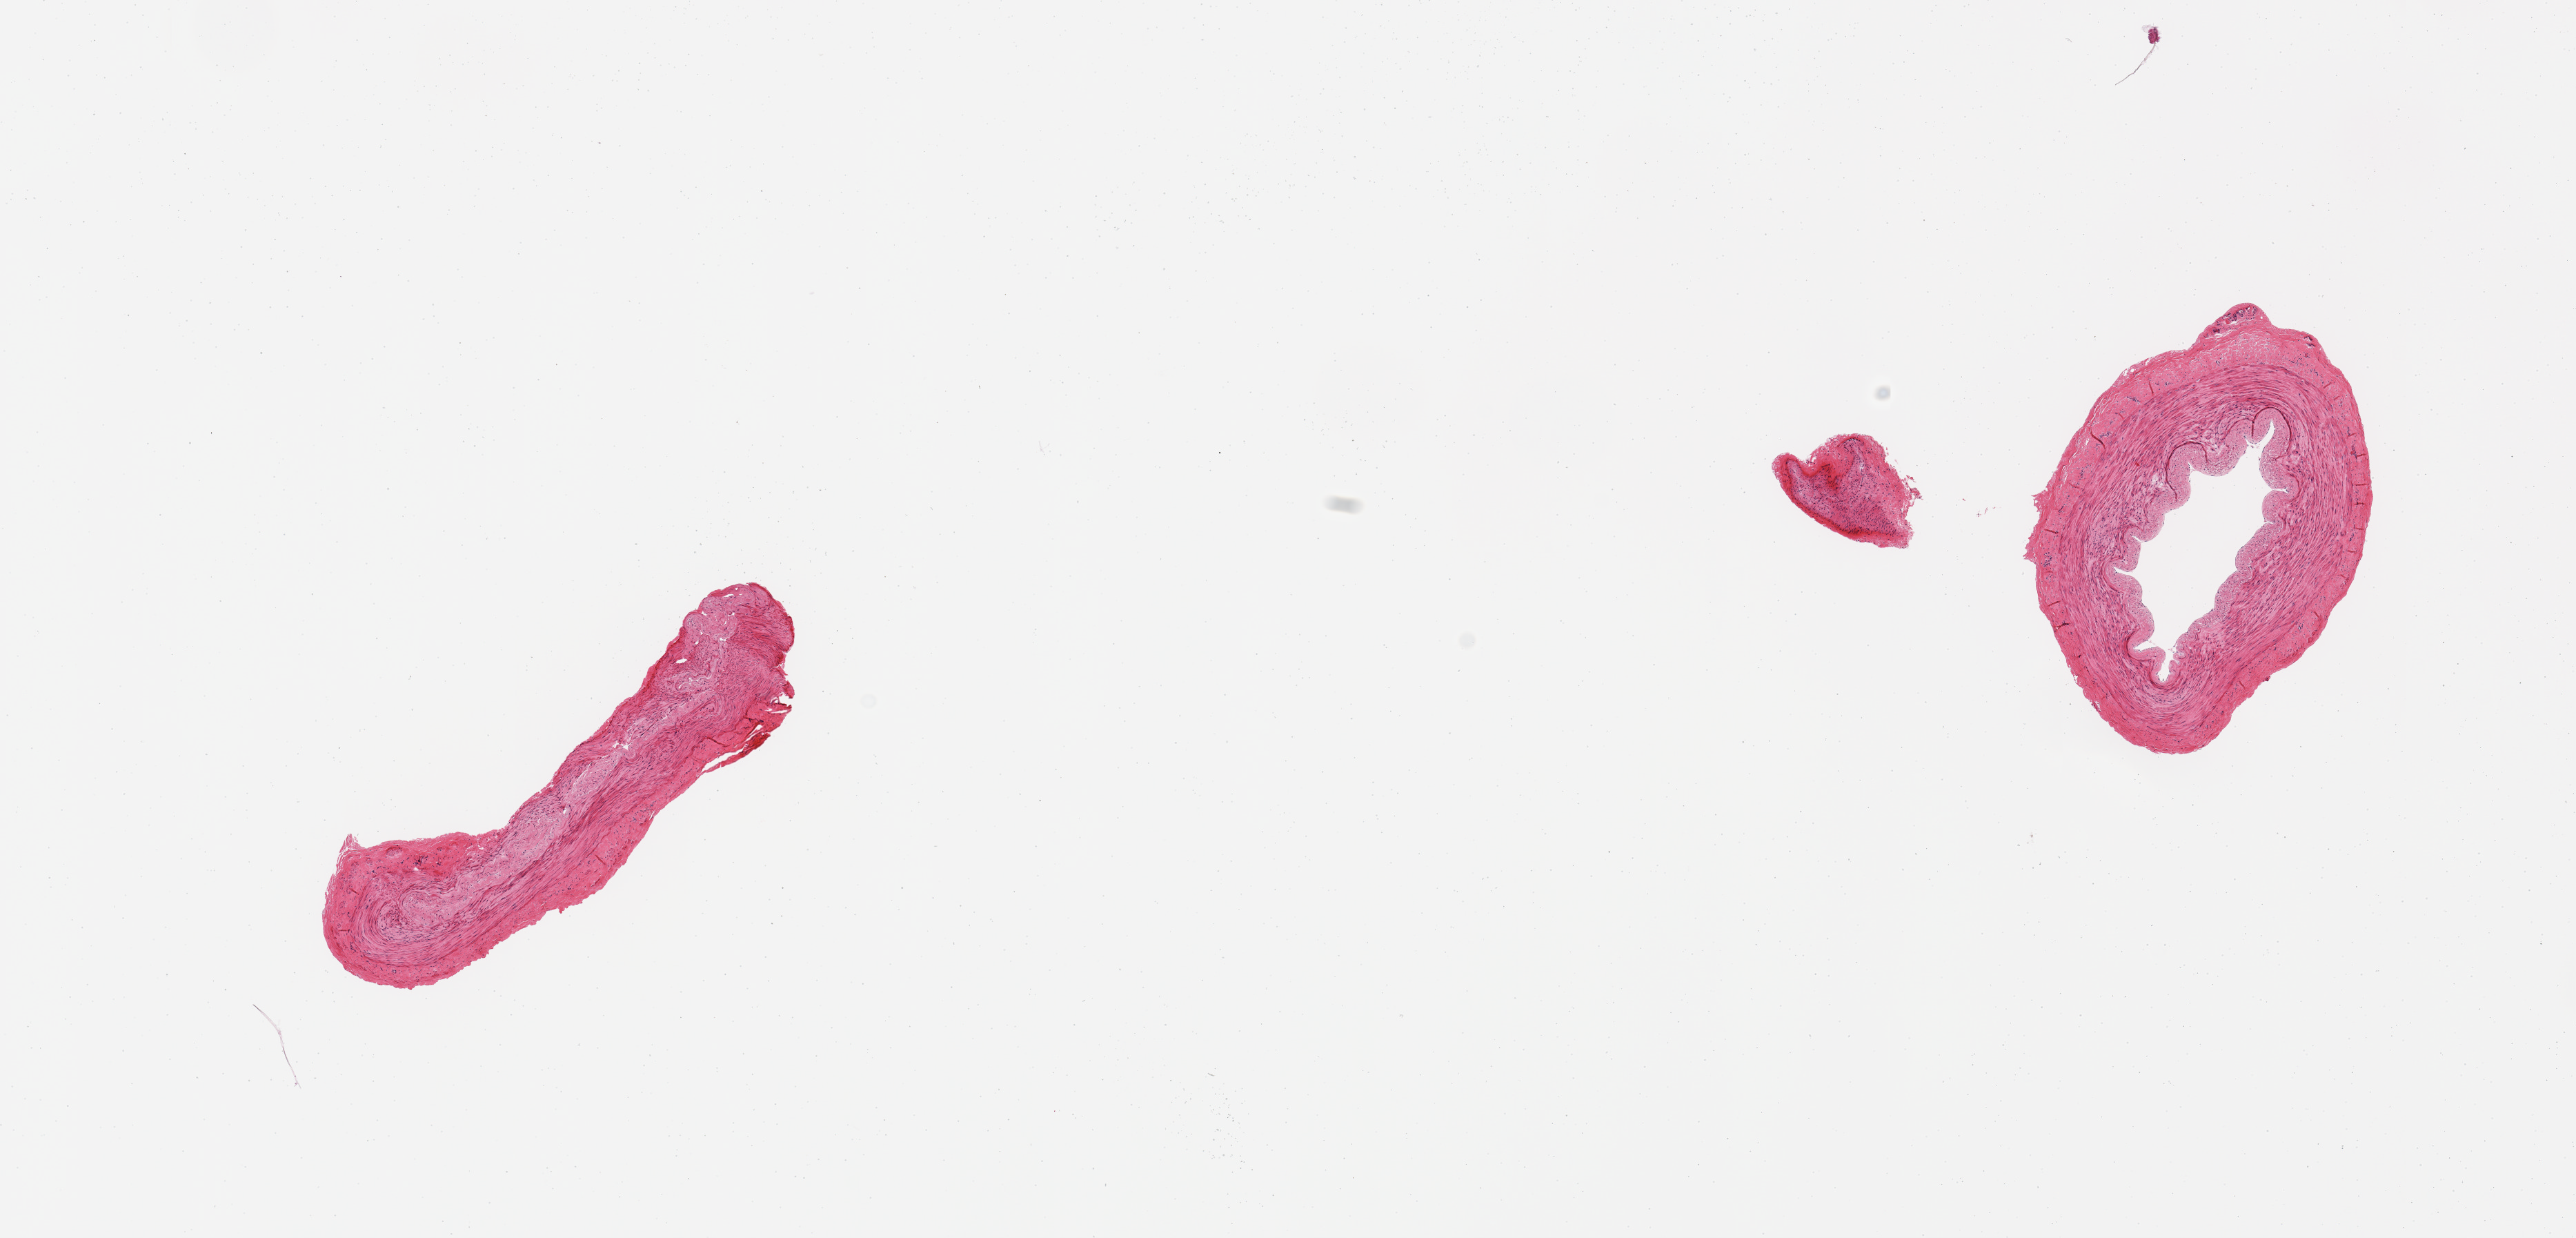
Digitized haematoxylin and eosin-stained section, low-resolution overview of the scanned area, about 14.8 x 7.1 mm, PAXgene-fixed paraffin-embedded (PFPE) section, section of tibial artery (target tissue), donor tissue sample.
Reviewer comment on this tissue sample: 2 pieces, no adherent fat or significant atherosis. One section disrupted.